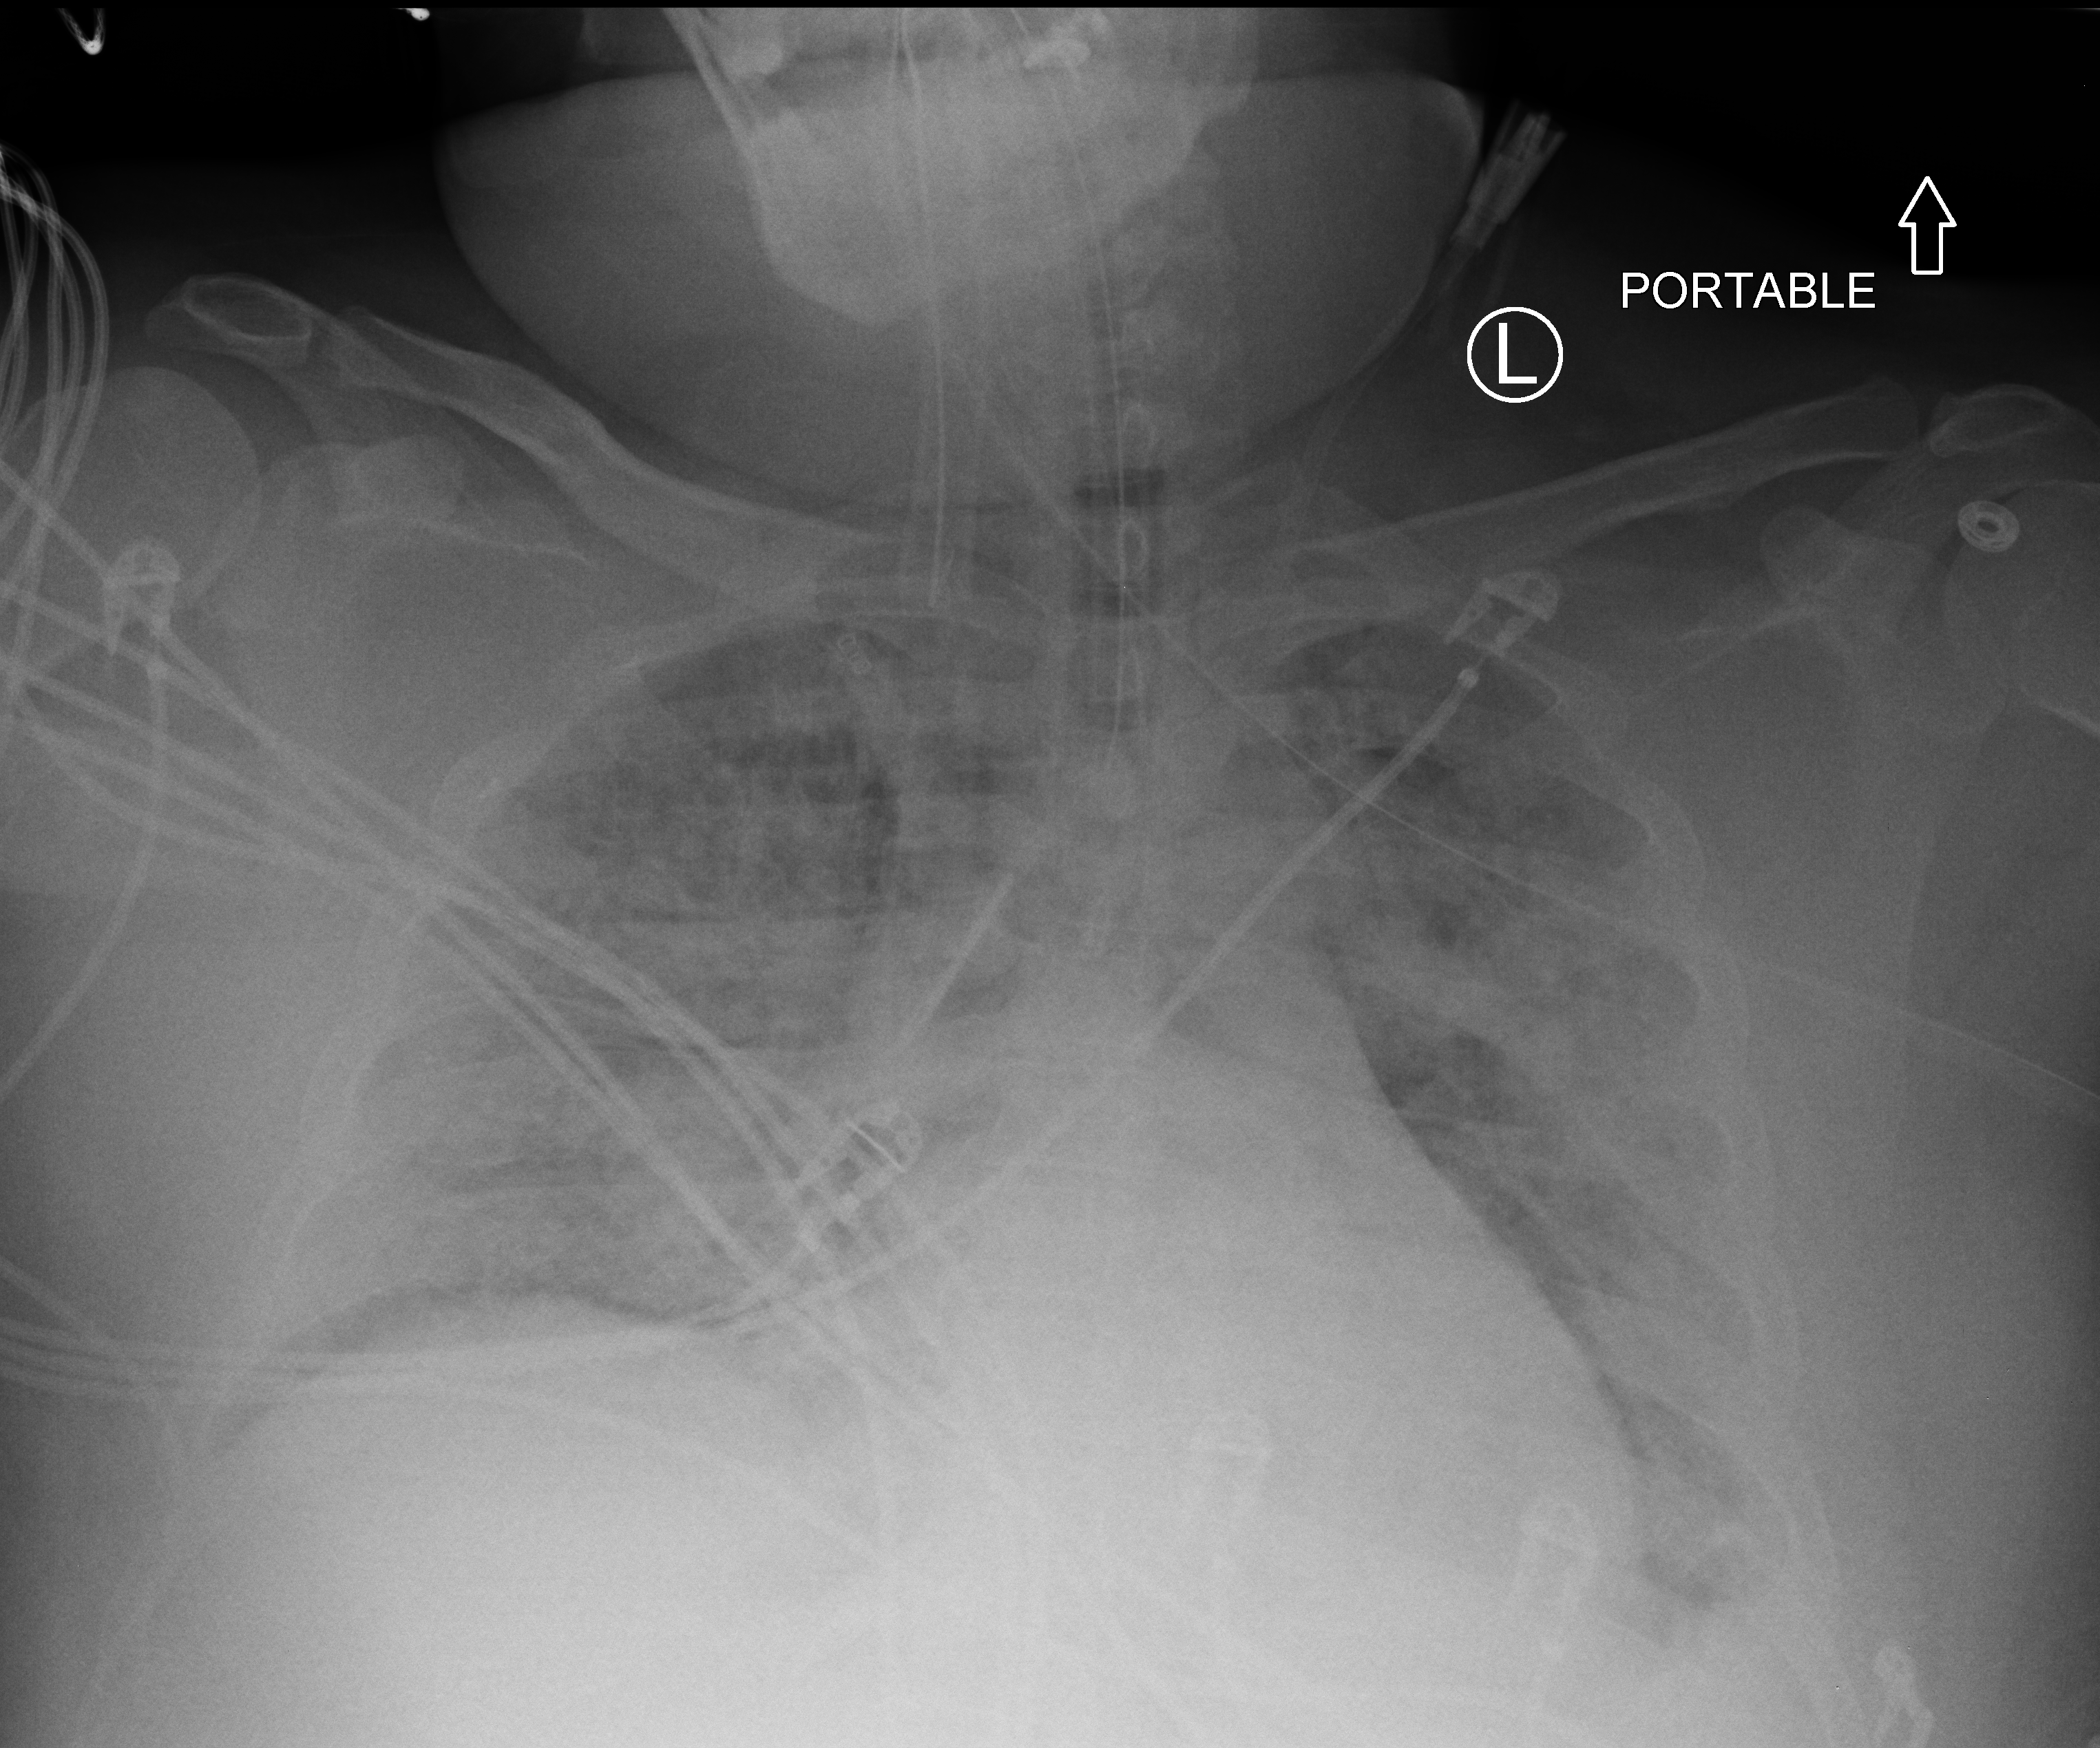
Chest X-ray (portable), anteroposterior (AP) projection. Adult patient hospitalised with COVID-19, age 18–59 years.
From the hospital-stay record, not from the radiograph (when in the stay this image was taken is not recorded):
- chronic kidney disease (admission record): no
- mechanically ventilated during this hospital stay: yes